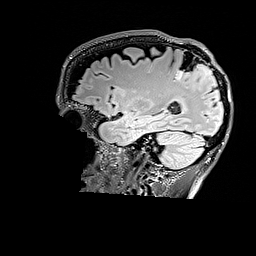
Brain MRI from a brain-tumour surgery series, one sagittal slice. Slice 119 of 176 in the series (ordered by position). T2 FLAIR. 1 mm slice thickness. 256 × 256 image matrix. Case-level facts recorded for this patient, not image findings: histopathology: Astrocytoma; WHO grade: 3.
Annotated regions visible in this slice (outlined manually by an expert reader):
- tumour: box from (x=175, y=64) to (x=212, y=80) px
- tumour: (x=205, y=68)–(x=212, y=81)